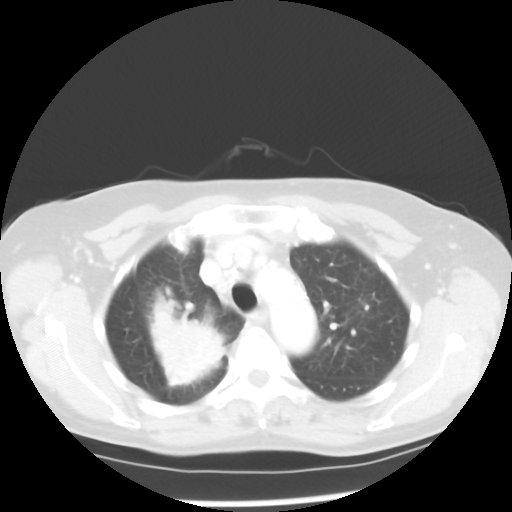
Chest CT, one axial slice; position 39 of 52 along the scan axis; reconstruction kernel STANDARD; lung window (W 1500 / L -600 HU); 5 mm slice thickness; 512 × 512 image matrix. Patient: female, 60 years. Case-level facts recorded for this patient, not image findings: clinical TNM (as recorded): T2 N1 M1a.
Structures marked on this image (rectangle marked by the reading radiologist):
- lung tumour (recorded histology: adenocarcinoma): bounding box [x1, y1, x2, y2] px = [145, 299, 229, 391]